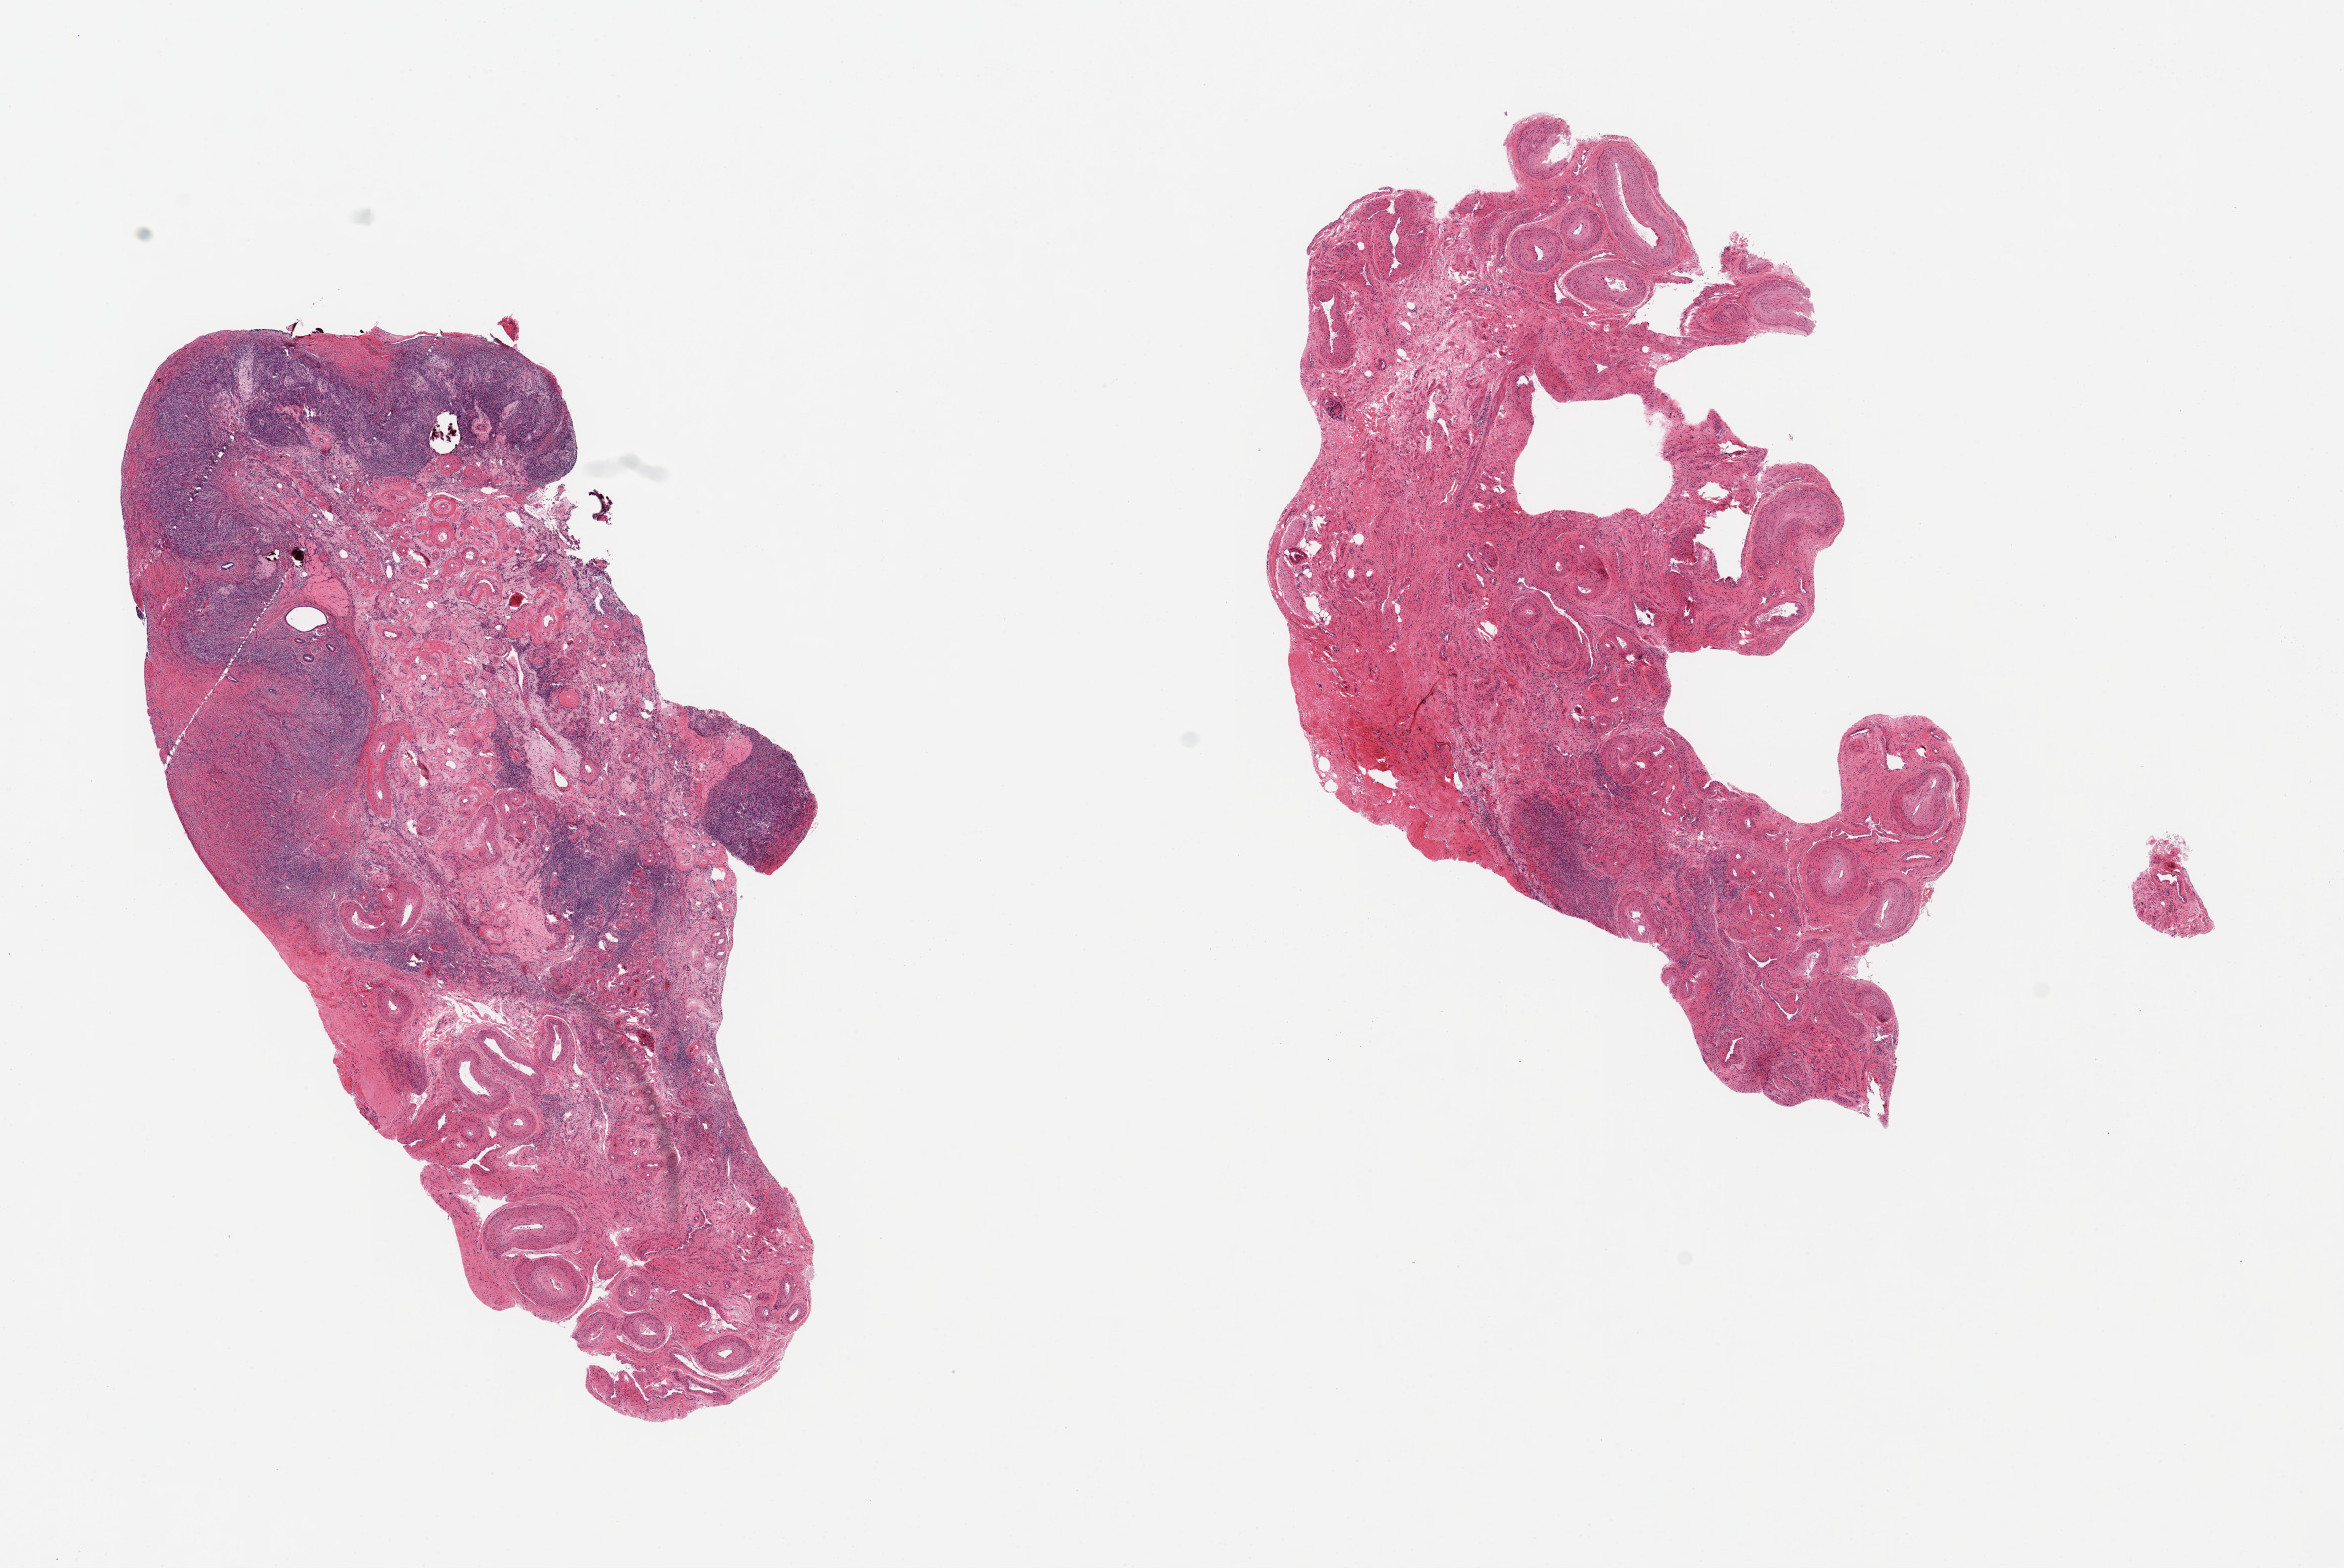
Whole-slide image, H&E stain, shown as a low-resolution overview of the whole scanned area (about 18.7 x 12.5 mm); PAXgene-fixed, paraffin-embedded tissue; section of ovary (target tissue); tissue donor sample. Donor sex: female.
Review note (as recorded): 2 pieces, typical post menopausal atrophy, prominent hilar vessels.